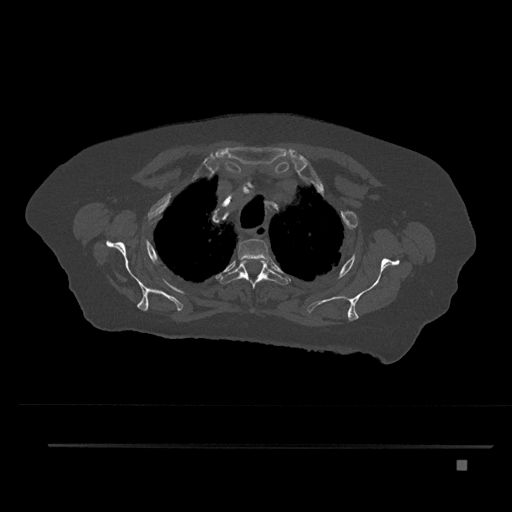
CT including the spine, one axial slice. Position 647 of 797 along the scan axis. Reconstruction kernel Br40s/3. 120 kVp. Bone window (W 1800 / L 400 HU). 0.5 mm slice thickness. 512 × 512 image matrix, field of view 437 × 437 mm. Female patient, age 76 years. Case-level facts recorded for this patient, not image findings: primary cancer: lung.
Structures marked on this image (semi-automatically segmented with operator editing):
- T2 vertebra: bounding box [x1, y1, x2, y2] px = [238, 239, 271, 272]
- T3 vertebra: [219, 258, 287, 288]